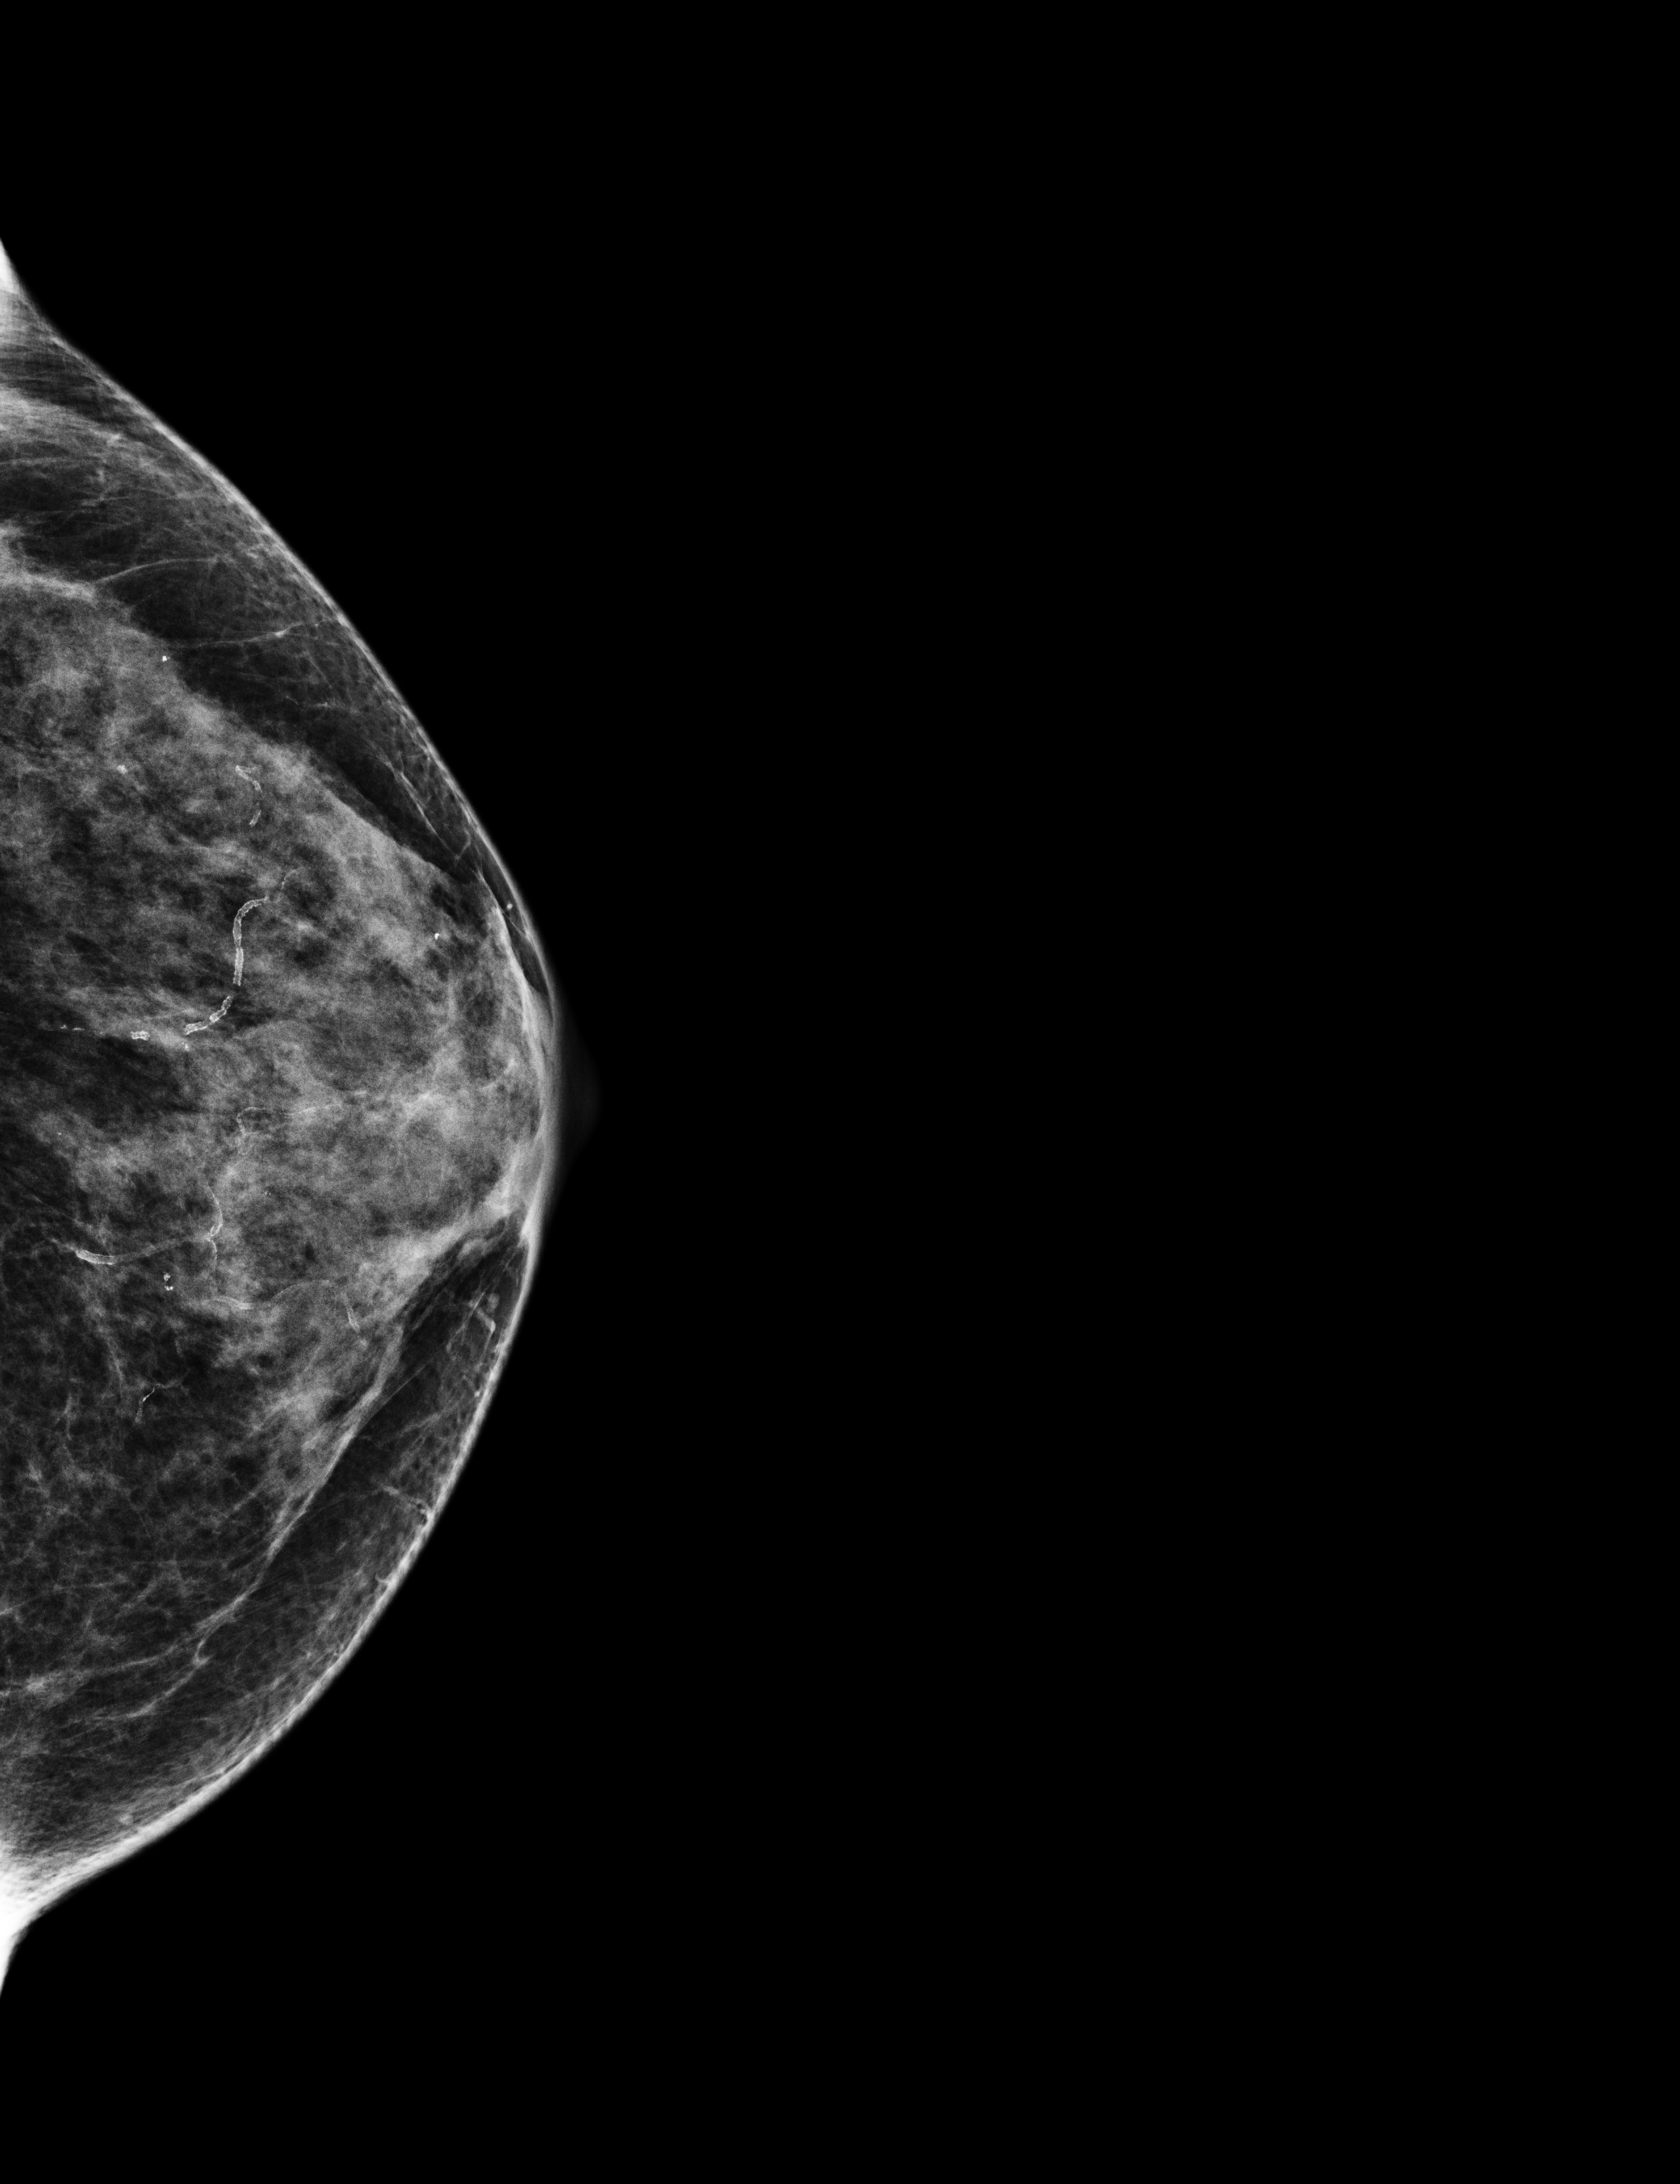
Screening examination; system: Selenia Dimensions. Female patient, age 65 years.
Image type: full-field digital mammogram. Breast: left. Projection: cranio-caudal projection.